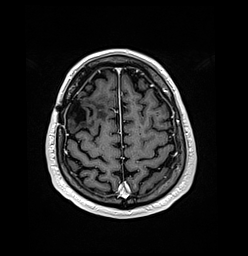
Brain MRI from a brain-tumour surgery series, one axial slice; position 37 of 176 along the scan axis; T1-weighted post-contrast; 1 mm slice thickness; 248 × 256 image matrix. From the clinical record (not read from this slice): histopathology: Oligodendroglioma; WHO grade: 3.
Structures marked on this image (expert manual segmentation):
- previous resection cavity: bounding box <68,95,87,124> (left, top, right, bottom; pixels)